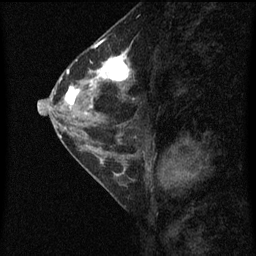
Breast MRI (dynamic contrast-enhanced), one sagittal slice; slice 30 of 60 in the series (ordered by position); dynamic contrast-enhanced series, image 2 of 4 at this slice position (ordered by acquisition); 1.5 T; TE 4.2 ms, TR 8 ms; 256 × 256 image matrix, field of view 180 × 180 mm. Patient: female, 56 years.
Outlined on this slice (semi-automatically segmented with operator editing):
- analysis volume of interest (the breast-tissue region the enhancement analysis was run in; not a lesion): box from (x=56, y=52) to (x=135, y=115) px
- tumour enhancement mask (voxels above the 70 % enhancement threshold inside the analysis volume of interest): (x=66, y=52)–(x=132, y=109)